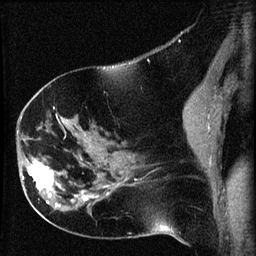
Breast MRI (dynamic contrast-enhanced), one sagittal slice. Slice 32 of 60 in the series (ordered by position). Dynamic contrast-enhanced series, image 2 of 3 at this slice position (ordered by acquisition). 1.5 T. TE 4.2 ms, TR 8.2 ms. 2 mm slice thickness. 256 × 256 image matrix. Female patient, age 63 years.
Outlined on this slice (semi-automatic segmentation, software-assisted and operator-edited):
- analysis volume of interest (the breast-tissue region the enhancement analysis was run in; not a lesion): box from (x=22, y=156) to (x=64, y=202) px
- tumour enhancement mask (voxels above the 70 % enhancement threshold inside the analysis volume of interest): (x=22, y=159)–(x=54, y=197)